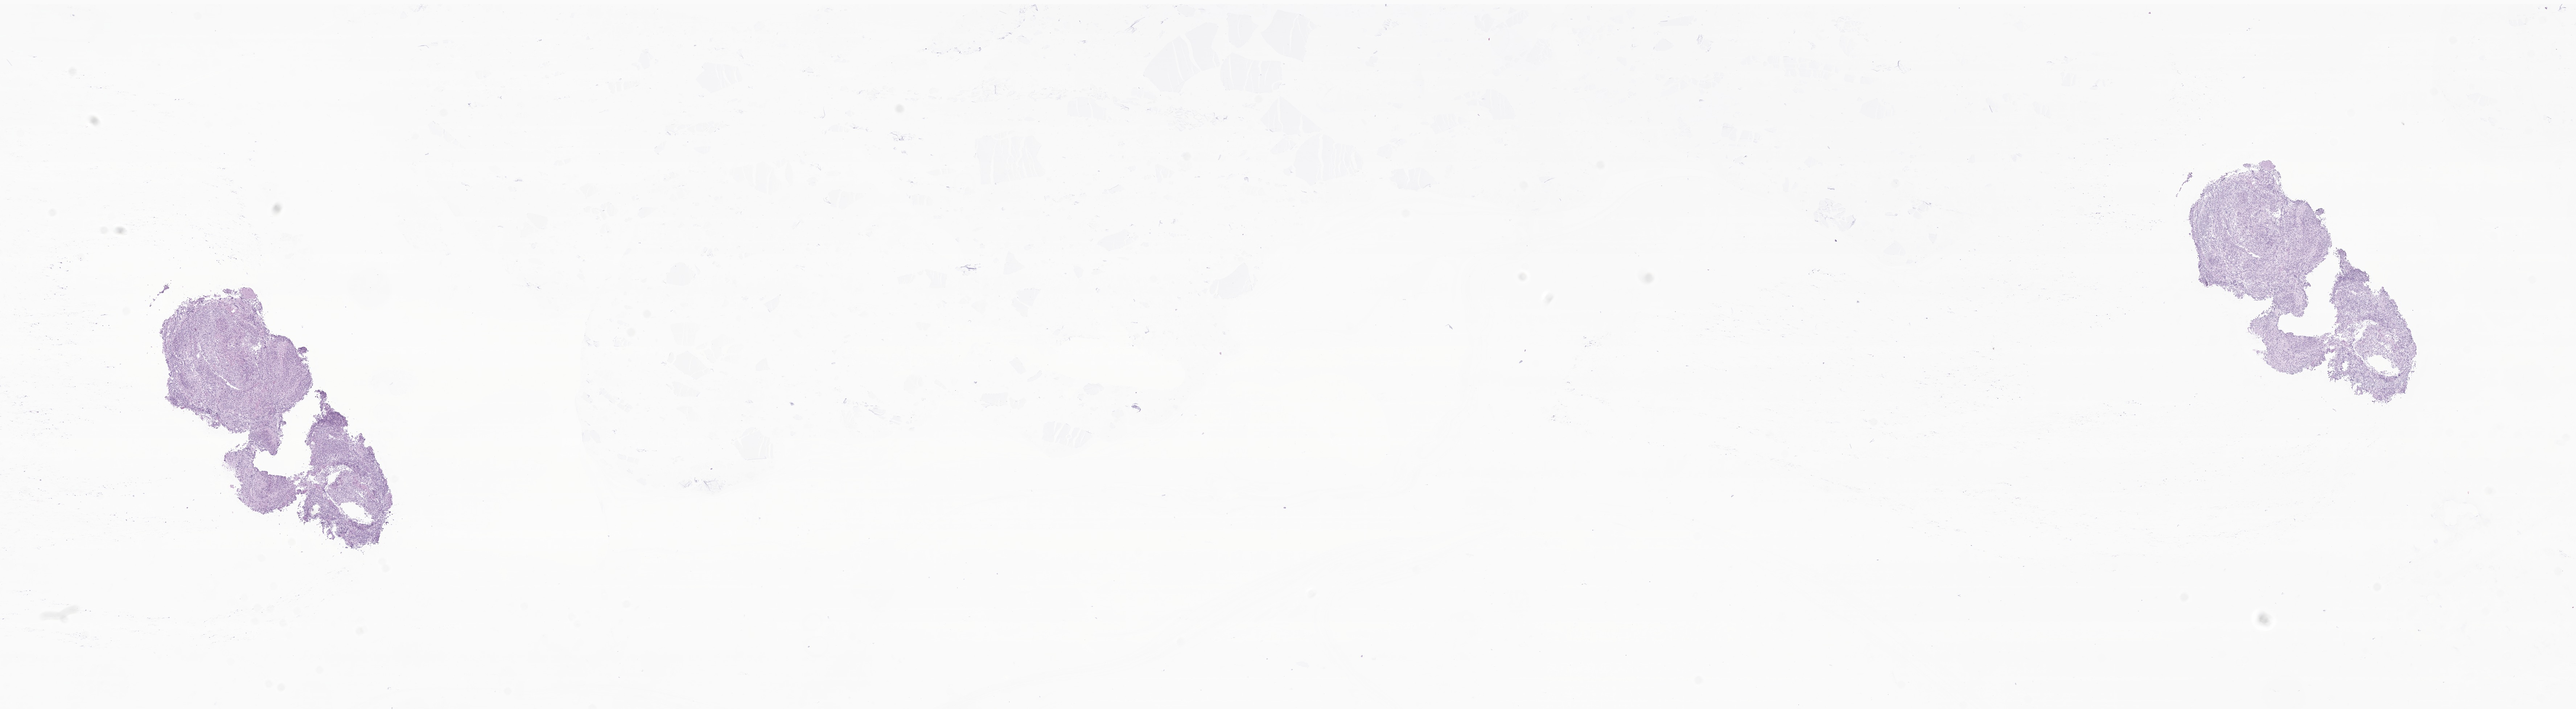
Digitized haematoxylin and eosin-stained section of tumor tissue from the brain, whole scanned area (about 29.9 x 8.2 mm) shown as a low-resolution overview. Frozen section (OCT-embedded). Patient: male, age 442 days (about 1.2 years).
Diagnosis (ICD-O-3 morphology term): Medulloblastoma, NOS.